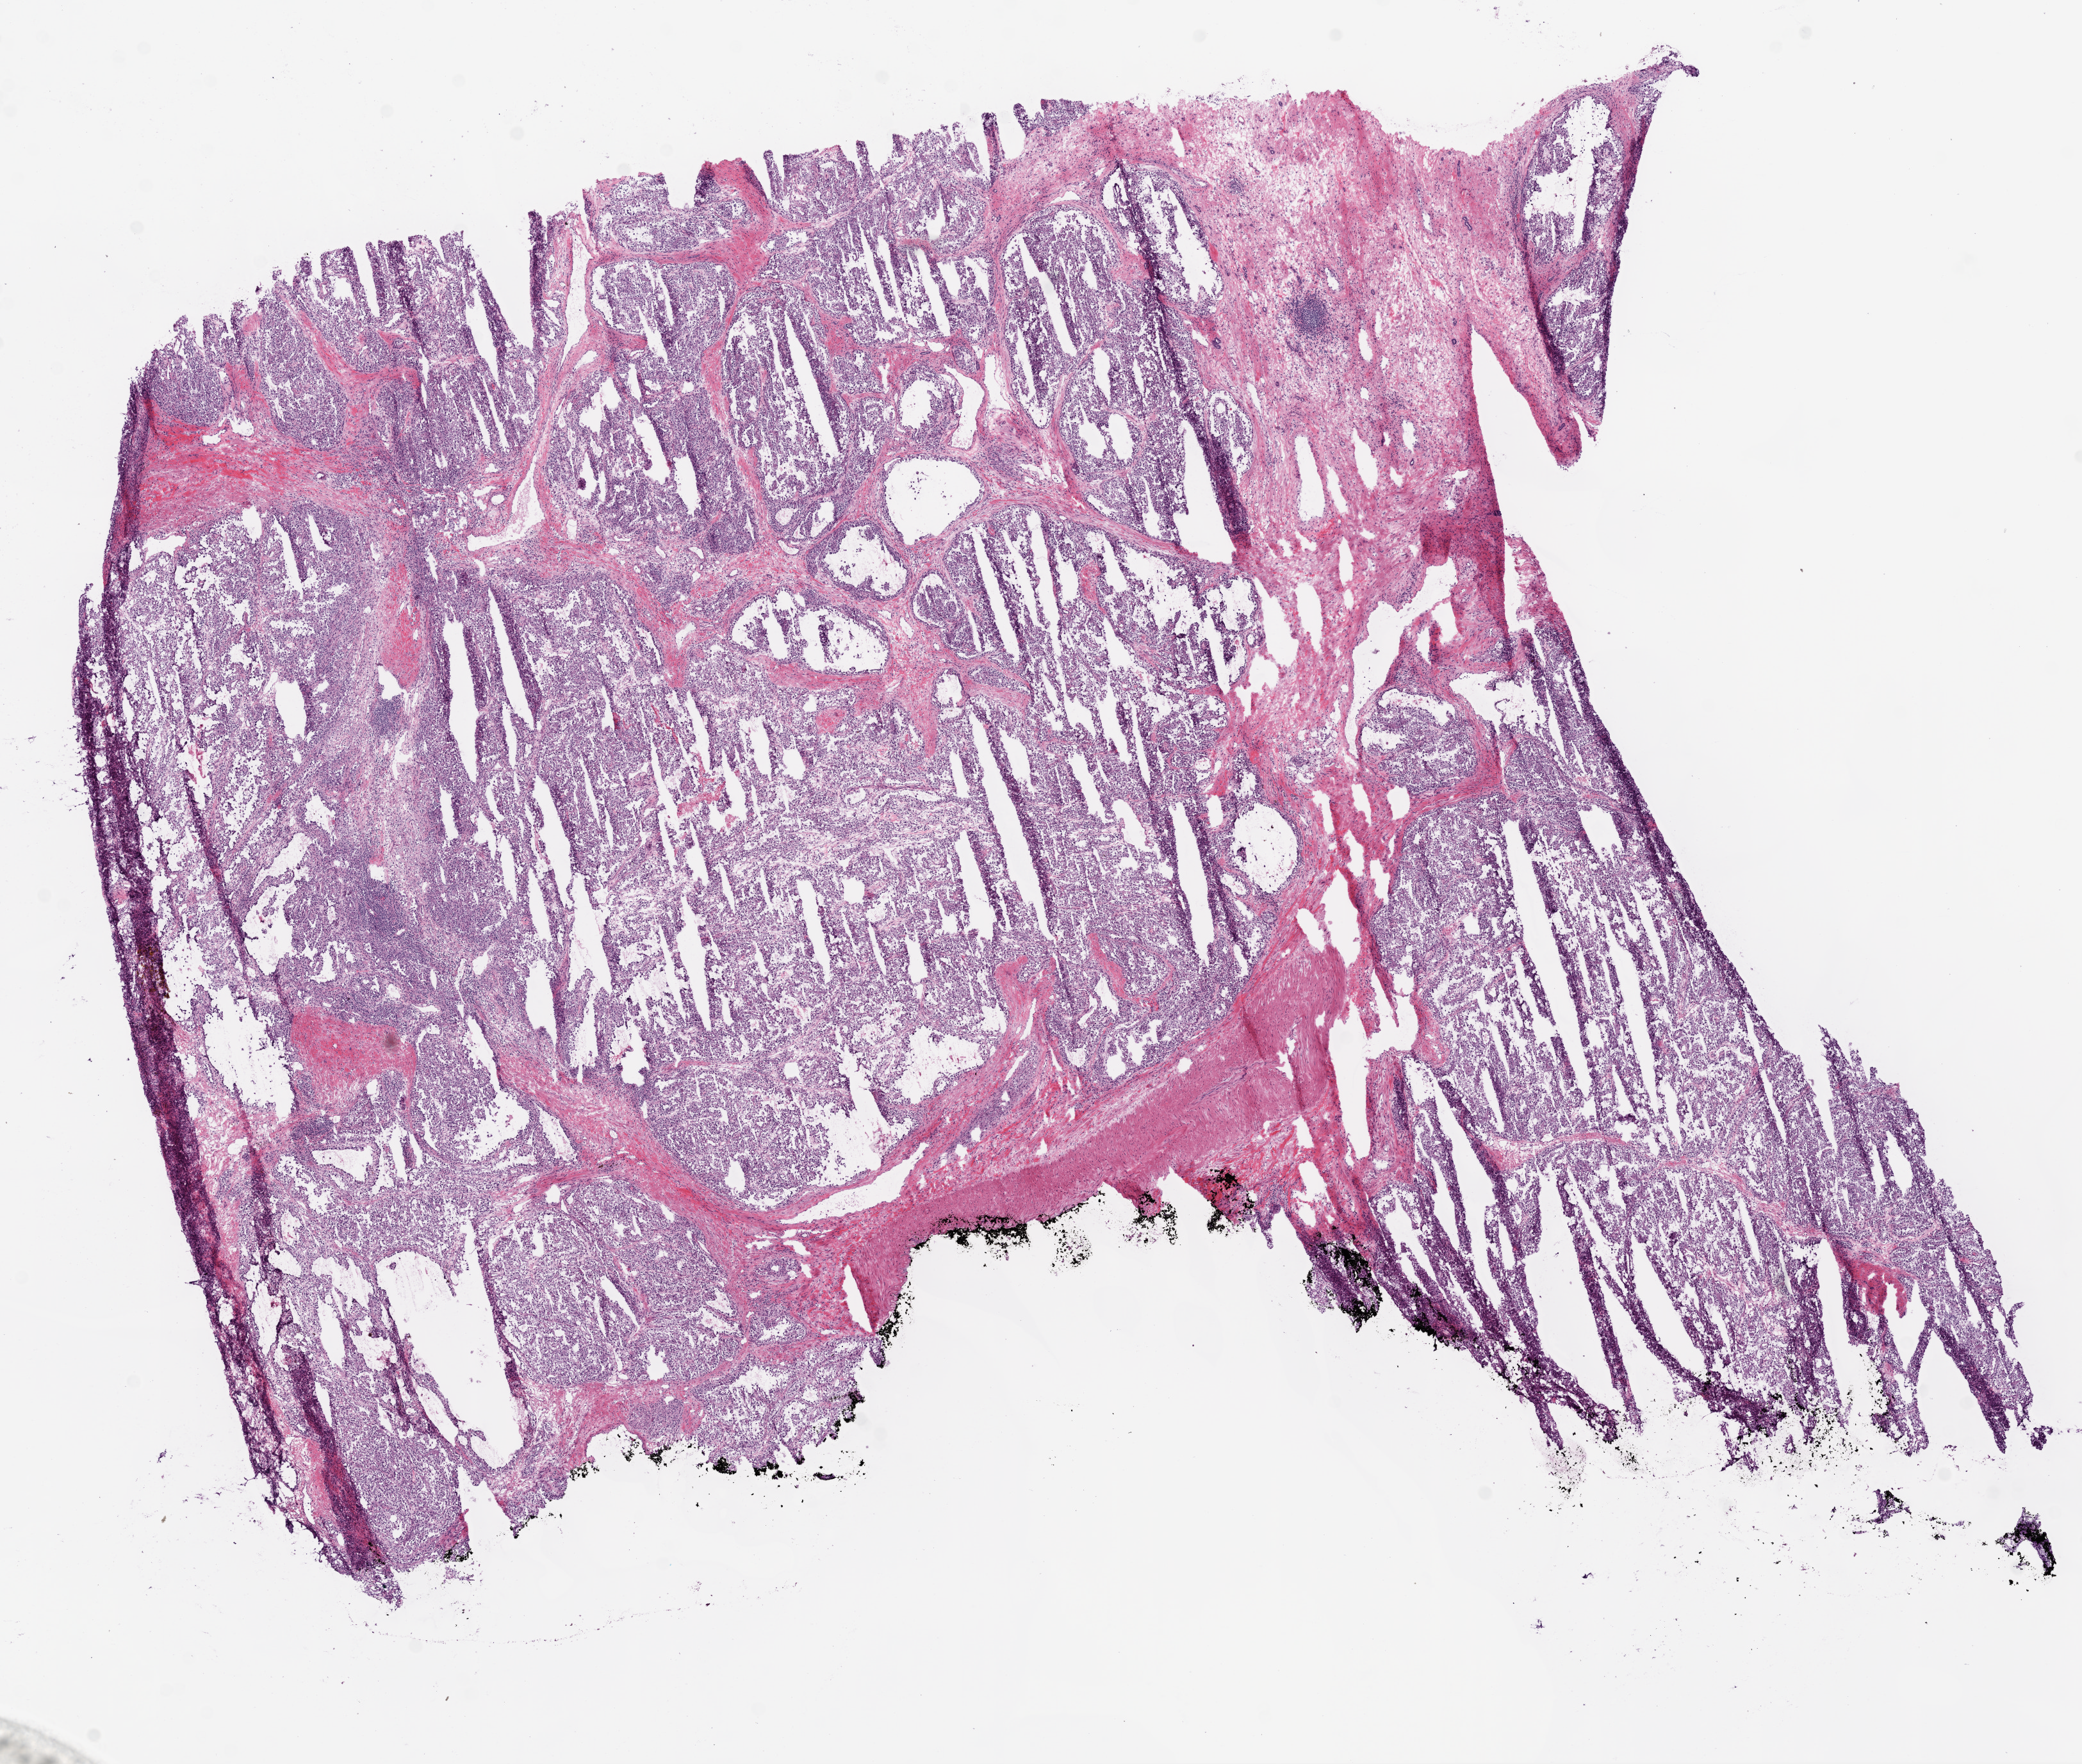
Hematoxylin and eosin (H&E) stained whole-slide image — a low-resolution overview of the entire scanned area, about 13.0 x 11.0 mm; frozen section; primary tumour sample from the kidney. Male patient; age at initial diagnosis 67 years. Histologic grade: G2 (moderately differentiated). Composition of this section per pathologist review: tumour cells 80%, tumour nuclei 80%, normal cells 10%, stromal cells 10%, necrosis 0%. Infiltration values recorded for this section: lymphocyte infiltration 3%, monocyte infiltration 0%, neutrophil infiltration 0%.
• diagnosis: Clear cell adenocarcinoma, NOS
• AJCC pathologic stage: II
• TNM: T2 N0 M0
• laterality: left